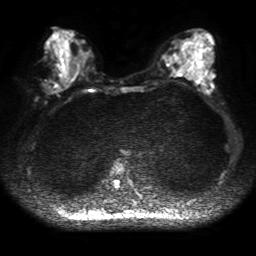
Breast MRI, one axial slice; slice 20 of 50 in the series (ordered by position); diffusion-weighted series; image 2 of 4 stored at this slice position (different b-values; order by instance number); 1.5 T; 4 mm slice thickness; 256 × 256 image matrix. Female patient.
Outlined on this slice (outlined manually by an expert reader):
- tumour on diffusion-weighted imaging: bounding box (x1, y1, x2, y2) in pixels: (44, 80, 60, 93)